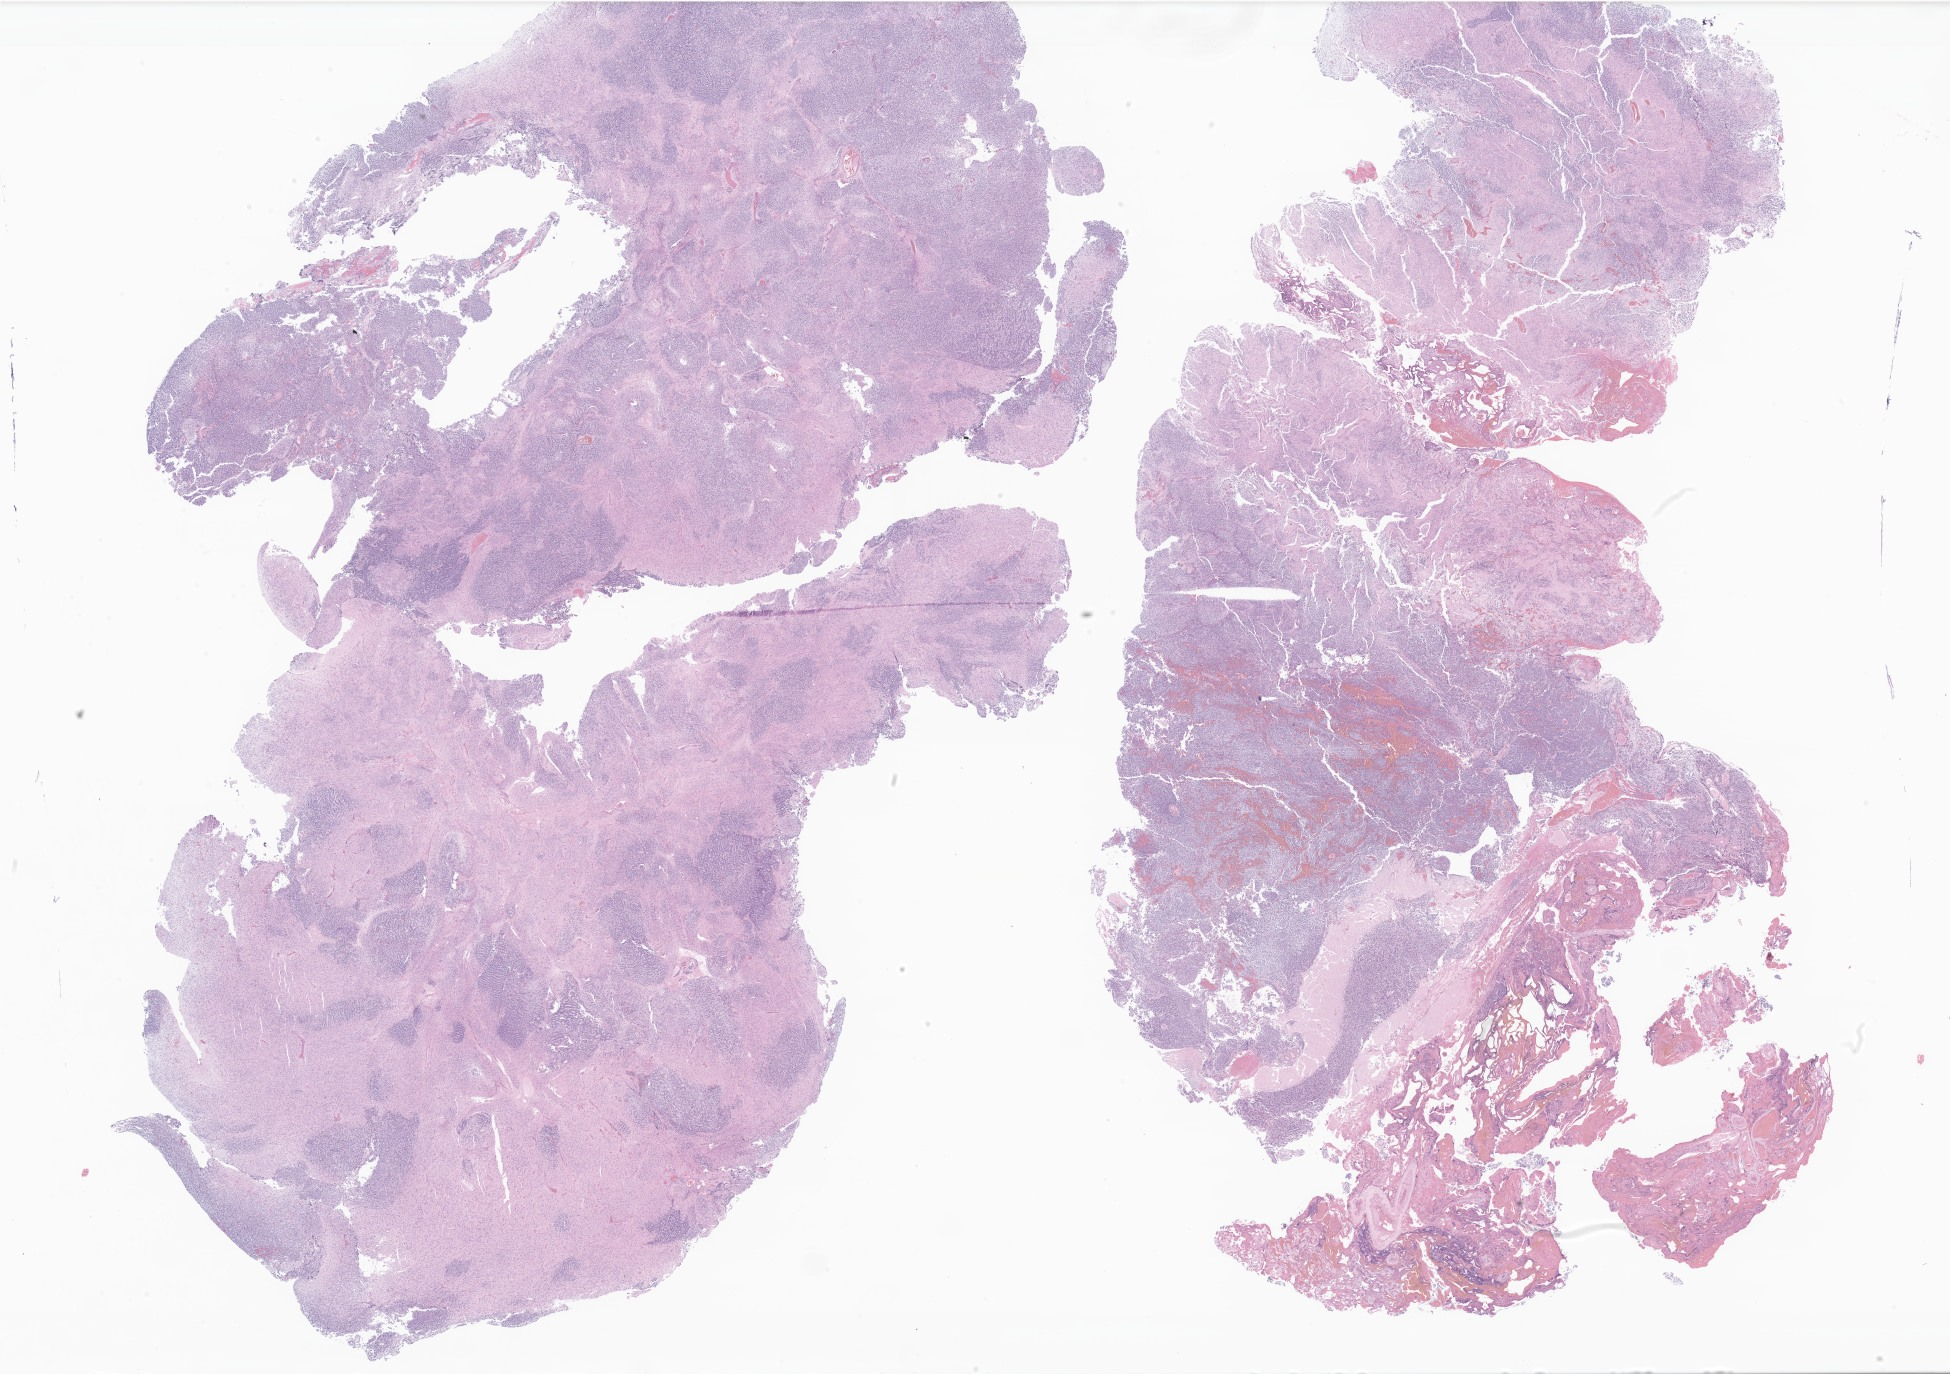
Digitized H&E-stained section of tumor tissue from the brain, a low-resolution overview of the entire scanned area, about 32.9 x 23.2 mm, formalin-fixed, paraffin-embedded (FFPE) tissue. Patient: male, age 121 months (10 years 1 month).
Diagnosis (ICD-O-3 morphology term): Medulloblastoma, NOS.